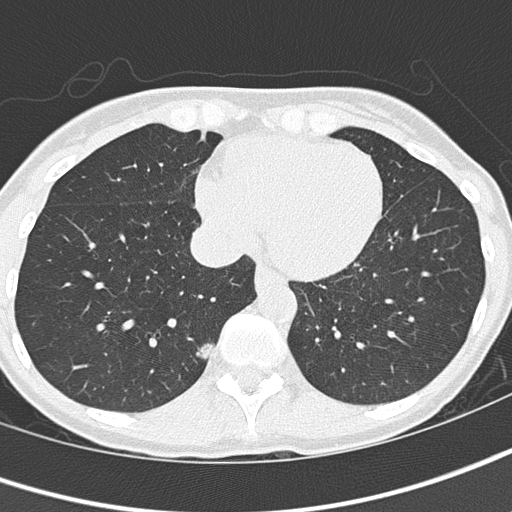
Low-dose screening chest CT, one axial slice. Position 45 of 145 along the scan axis. Reconstruction kernel B50f. 120 kVp. Lung window (W 1500 / L -600 HU). 2 mm slice thickness. 512 × 512 image matrix, field of view 276 × 276 mm.
Structures marked on this image (outlined manually by an expert reader):
- lesion 1 (tumor, lower lobe of right lung): box from (x=192, y=339) to (x=213, y=359) px